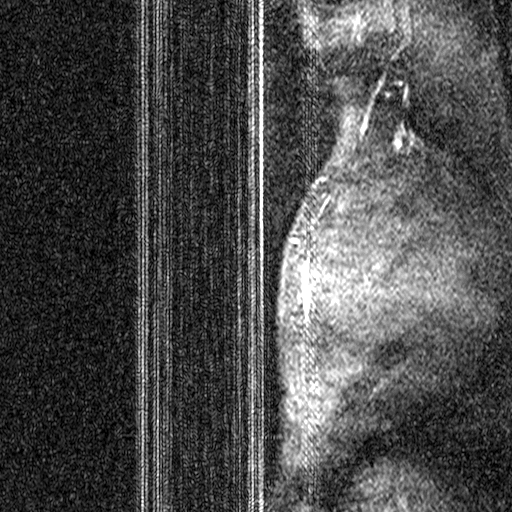
Breast MRI (dynamic contrast-enhanced), one sagittal slice; position 36 of 44 along the scan axis; dynamic contrast-enhanced study with each time point stored as its own series, time point 2 of 3 at this slice position (early post-contrast, ordered by acquisition time); 1.5 T; TE 4.5 ms, TR 11 ms; 3 mm slice thickness; 512 × 512 image matrix. Female patient, age 44 years. Case-level facts recorded for this patient, not image findings: setting: breast cancer imaged before/during neoadjuvant chemotherapy; receptor status: HR-positive, HER2-negative.
Outlined on this slice (semi-automatically segmented with operator editing):
- analysis volume of interest (the breast-tissue region the enhancement analysis was run in; not a lesion): box from (x=206, y=164) to (x=319, y=299) px
- tumour enhancement mask (voxels above the 90 % enhancement threshold inside the analysis volume of interest): (x=260, y=165)–(x=314, y=272)